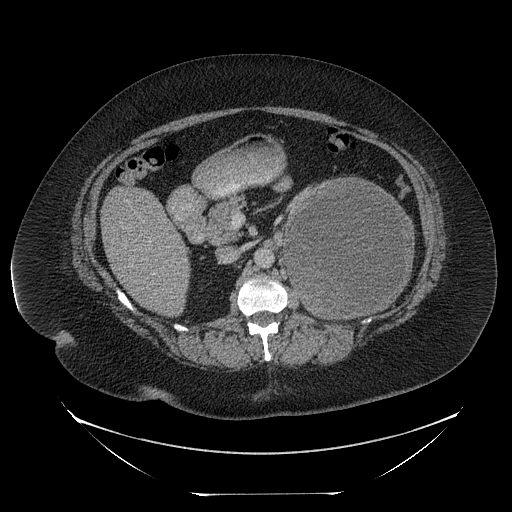
Contrast-enhanced abdominal CT, one axial slice; slice 133 of 205 in the series (ordered by position); reconstruction kernel STANDARD; intravenous contrast given; soft-tissue window (W 400 / L 40 HU); 512 × 512 image matrix. Patient: female, 53 years. Case-level facts recorded for this patient, not image findings: diagnosis: adrenocortical carcinoma; tumour side: left adrenal; tumour size at pathology: 17 cm.
Annotated regions visible in this slice (semi-automatic segmentation, software-assisted and operator-edited):
- mass: bounding box (x1, y1, x2, y2) in pixels: (284, 179, 413, 319)